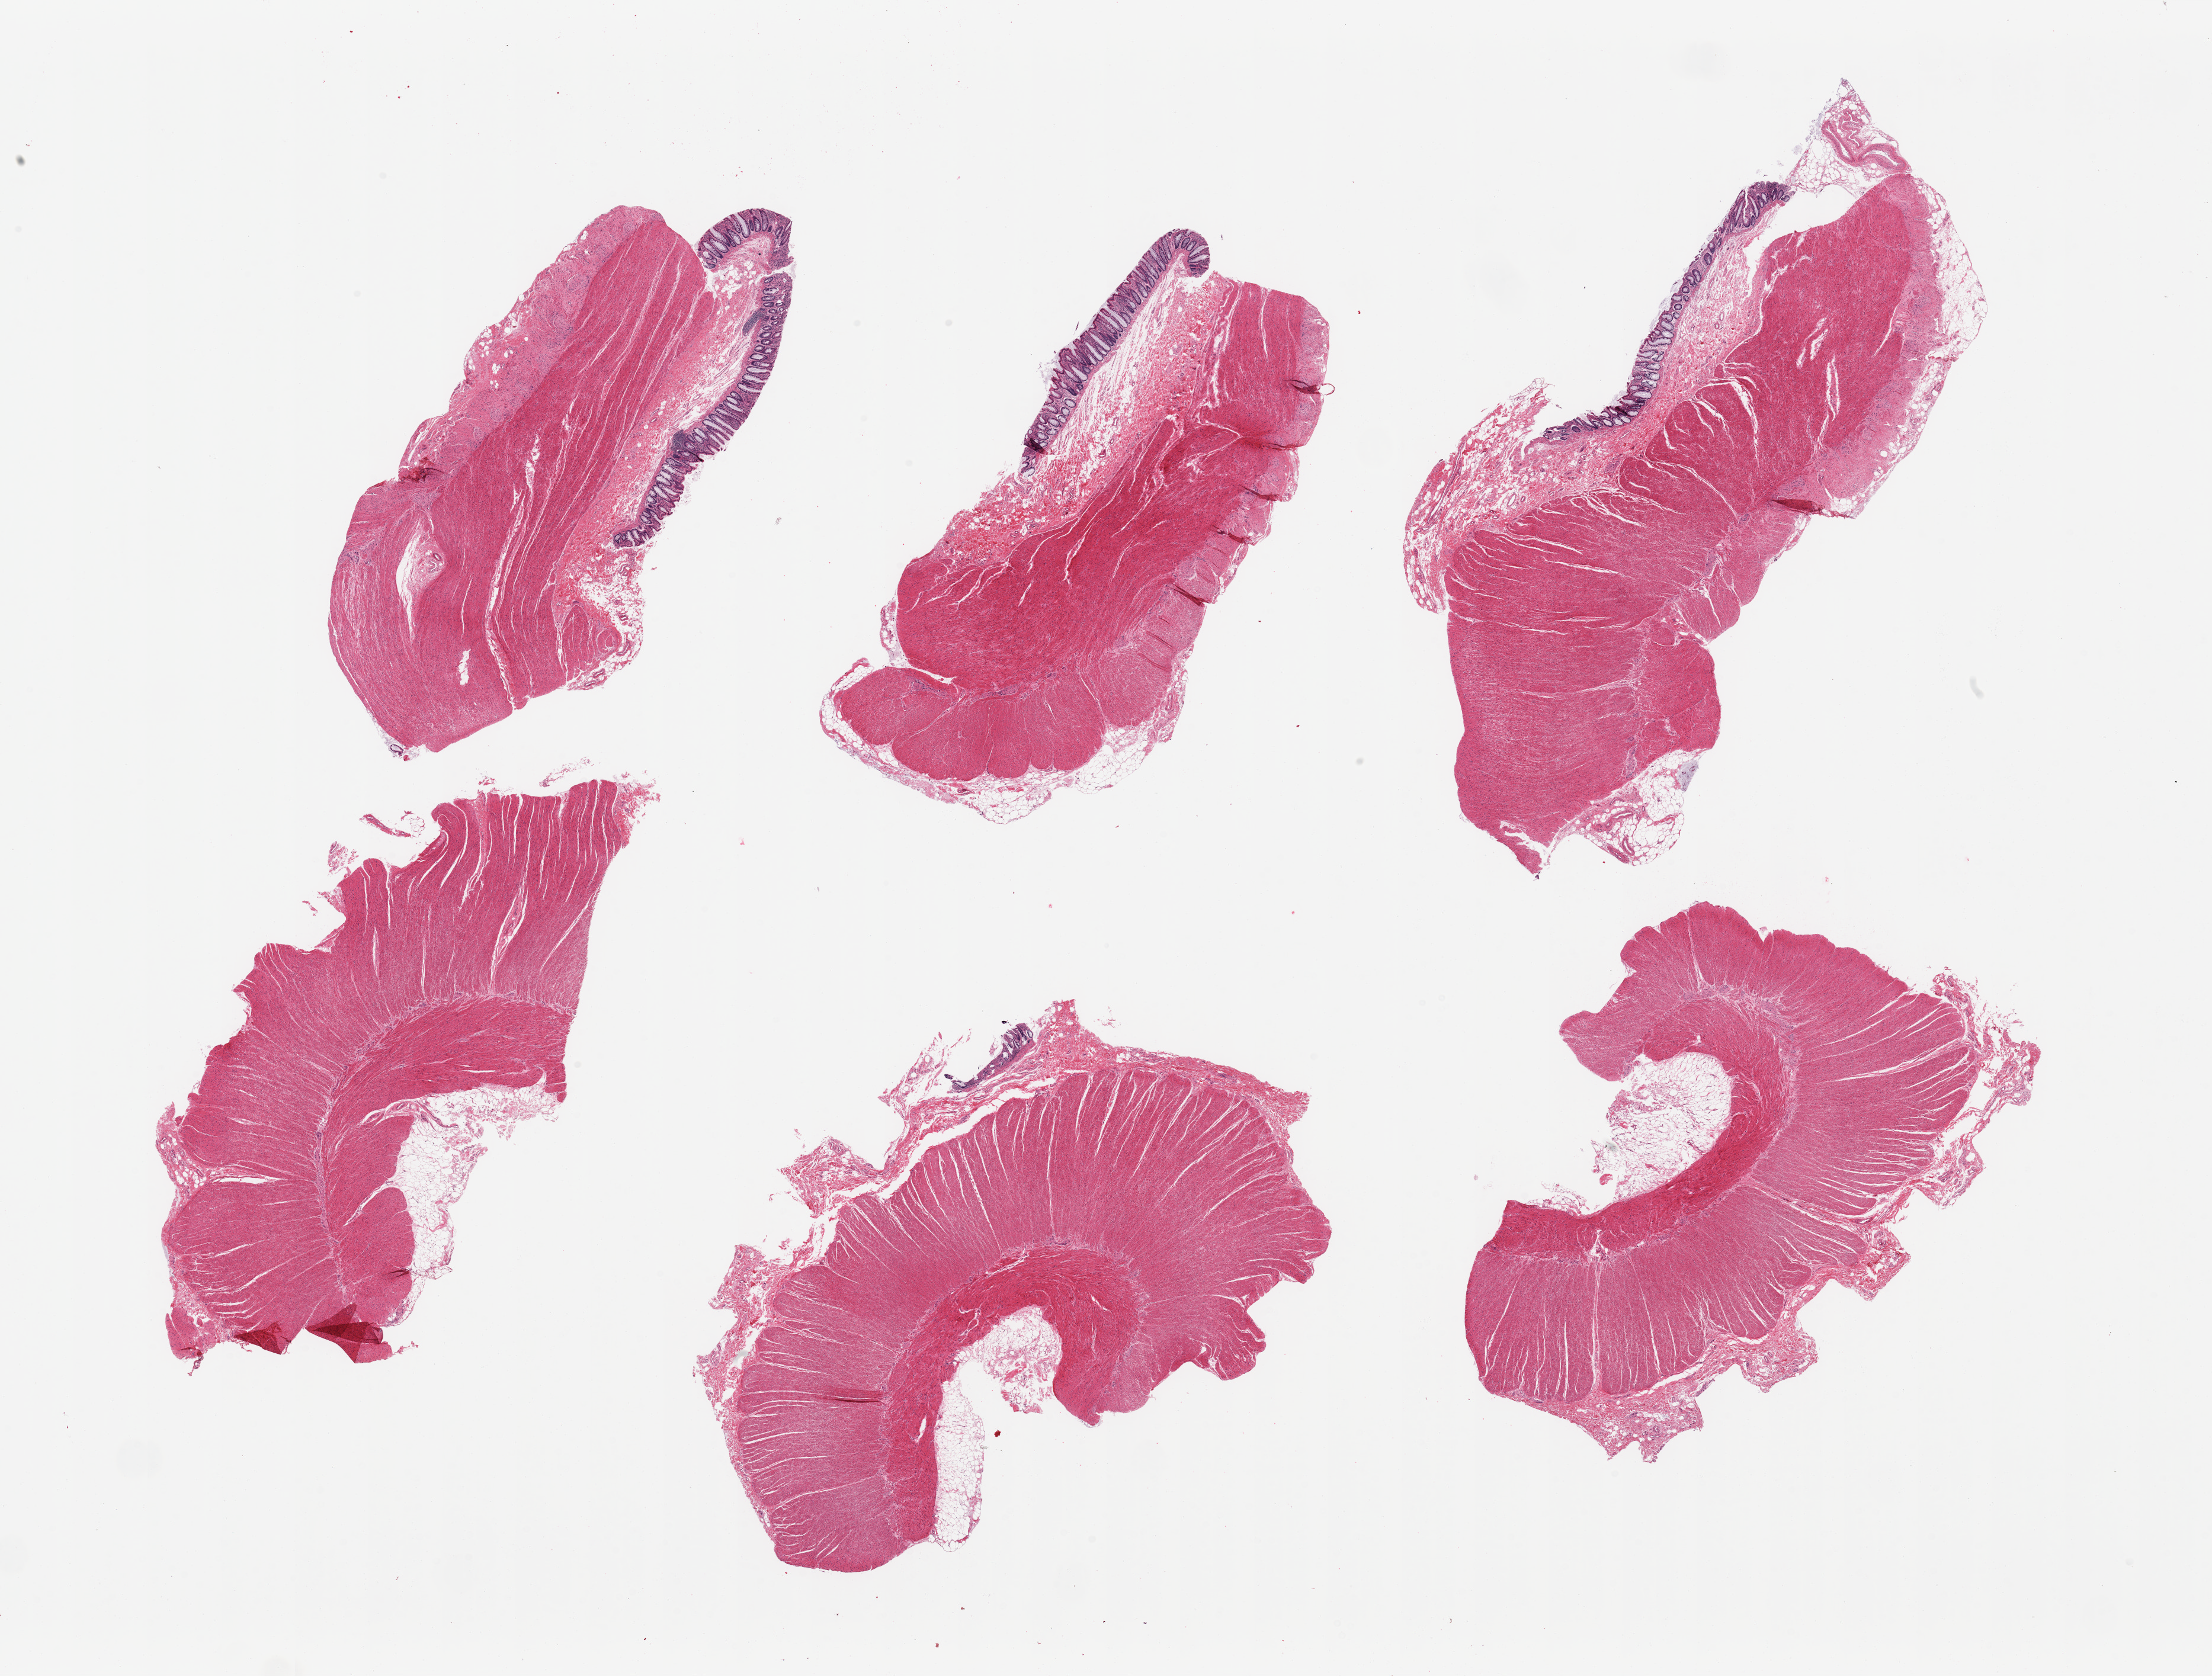
Digitized haematoxylin and eosin-stained section, brightfield, low-resolution overview of the scanned area, about 29.5 x 22.4 mm. Donor: female.
- specimen: PAXgene-fixed paraffin-embedded (PFPE) section; target tissue: sigmoid colon; donor tissue sample